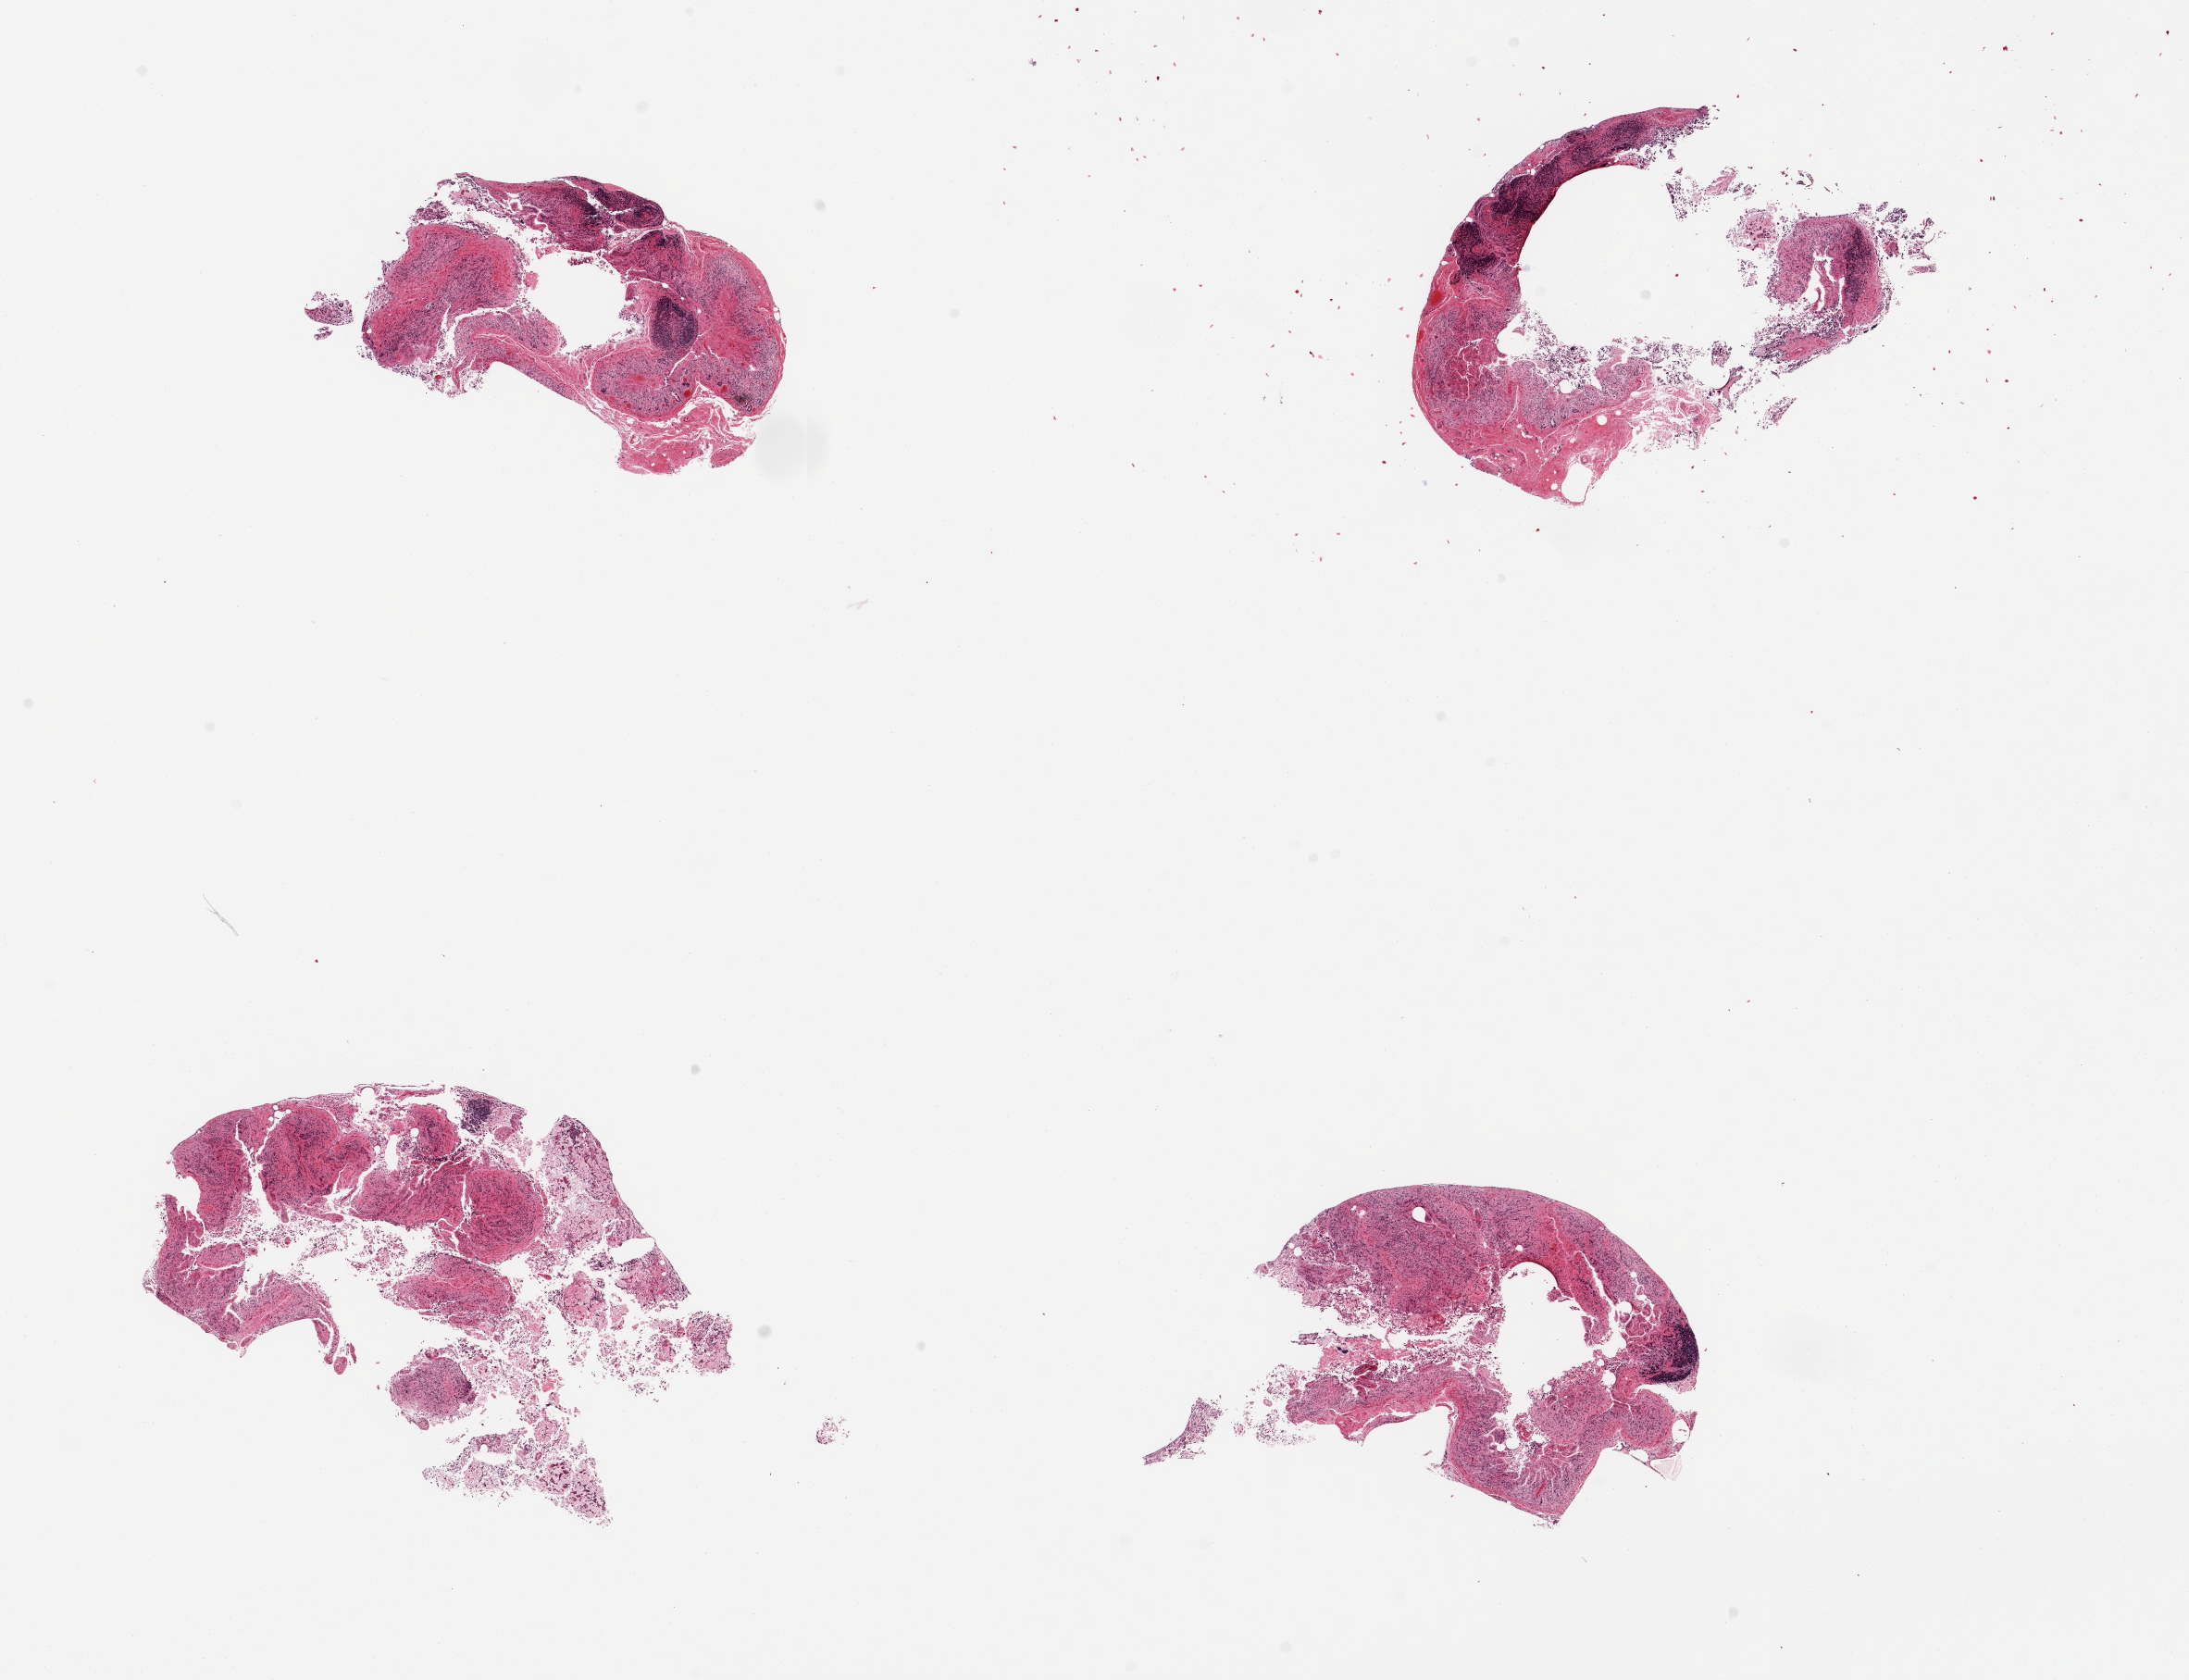
Whole-slide image, hematoxylin and eosin (H&E) stain — whole scanned area (about 18.7 x 14.4 mm, from a 20x scan) shown as a low-resolution overview; PAXgene-fixed paraffin-embedded (PFPE) section; target tissue: ileum; tissue donor sample. Male donor.
Pathologist's review note for this sample: 4 pieces, glandular mucosa autolyzed; residual lymphoid aggregates are ~~20% of tissue.